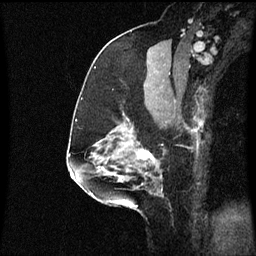
Breast MRI (dynamic contrast-enhanced), one sagittal slice. Position 36 of 60 along the scan axis. Dynamic contrast-enhanced series, image 2 of 3 at this slice position (ordered by acquisition). 1.5 T. TE 4.2 ms, TR 8.9 ms. 2 mm slice thickness. 256 × 256 image matrix, field of view 200 × 200 mm. Patient: female, 58 years. From the clinical record (not read from this slice): setting: breast cancer imaged before/during neoadjuvant chemotherapy; receptor status: triple-negative.
Structures marked on this image (semi-automatically segmented with operator editing):
- analysis volume of interest (the breast-tissue region the enhancement analysis was run in; not a lesion): bounding box (x1, y1, x2, y2) in pixels: (104, 118, 171, 179)
- tumour enhancement mask (voxels above the 70 % enhancement threshold inside the analysis volume of interest): (104, 150, 155, 171)